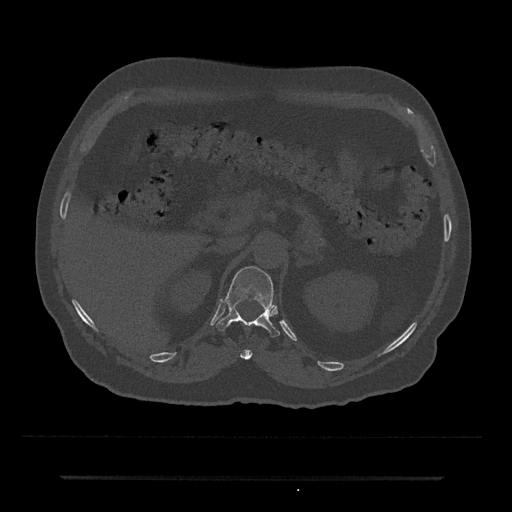
CT including the spine, one axial slice. Slice 136 of 797 in the series (ordered by position). Reconstruction kernel Br40s/3. 120 kVp. Bone window (W 1800 / L 400 HU). 512 × 512 image matrix. Patient: male, 69 years. Case-level facts recorded for this patient, not image findings: primary cancer: prostate.
Outlined on this slice (semi-automatic segmentation, software-assisted and operator-edited):
- T11 vertebra: box from (x=240, y=349) to (x=252, y=360) px
- T12 vertebra: (x=216, y=266)–(x=280, y=338)